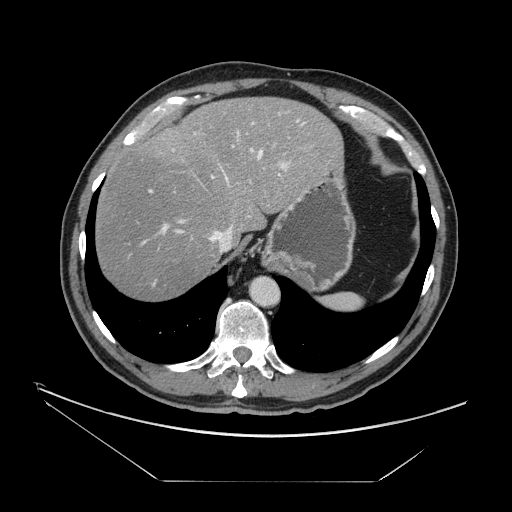
Contrast-enhanced abdominal CT, one axial slice. Slice 124 of 161 in the series (ordered by position). Reconstruction kernel STANDARD. Intravenous contrast given. Soft-tissue window (W 400 / L 40 HU). 512 × 512 image matrix, field of view 440 × 440 mm. Male patient, age 65 years. From the clinical record (not read from this slice): diagnosis: colorectal cancer liver metastases, imaged before liver resection; multiple liver metastases: yes; largest metastasis: 4.2 cm; disease in both lobes: yes.
Annotated regions visible in this slice (manually delineated by an expert):
- hepatic veins: bounding box [x1, y1, x2, y2] px = [175, 134, 264, 252]
- liver: [95, 97, 342, 300]
- planned liver remnant (the part of the liver to remain after resection): [95, 97, 342, 301]
- portal vein (with intrahepatic branches): [149, 111, 307, 235]